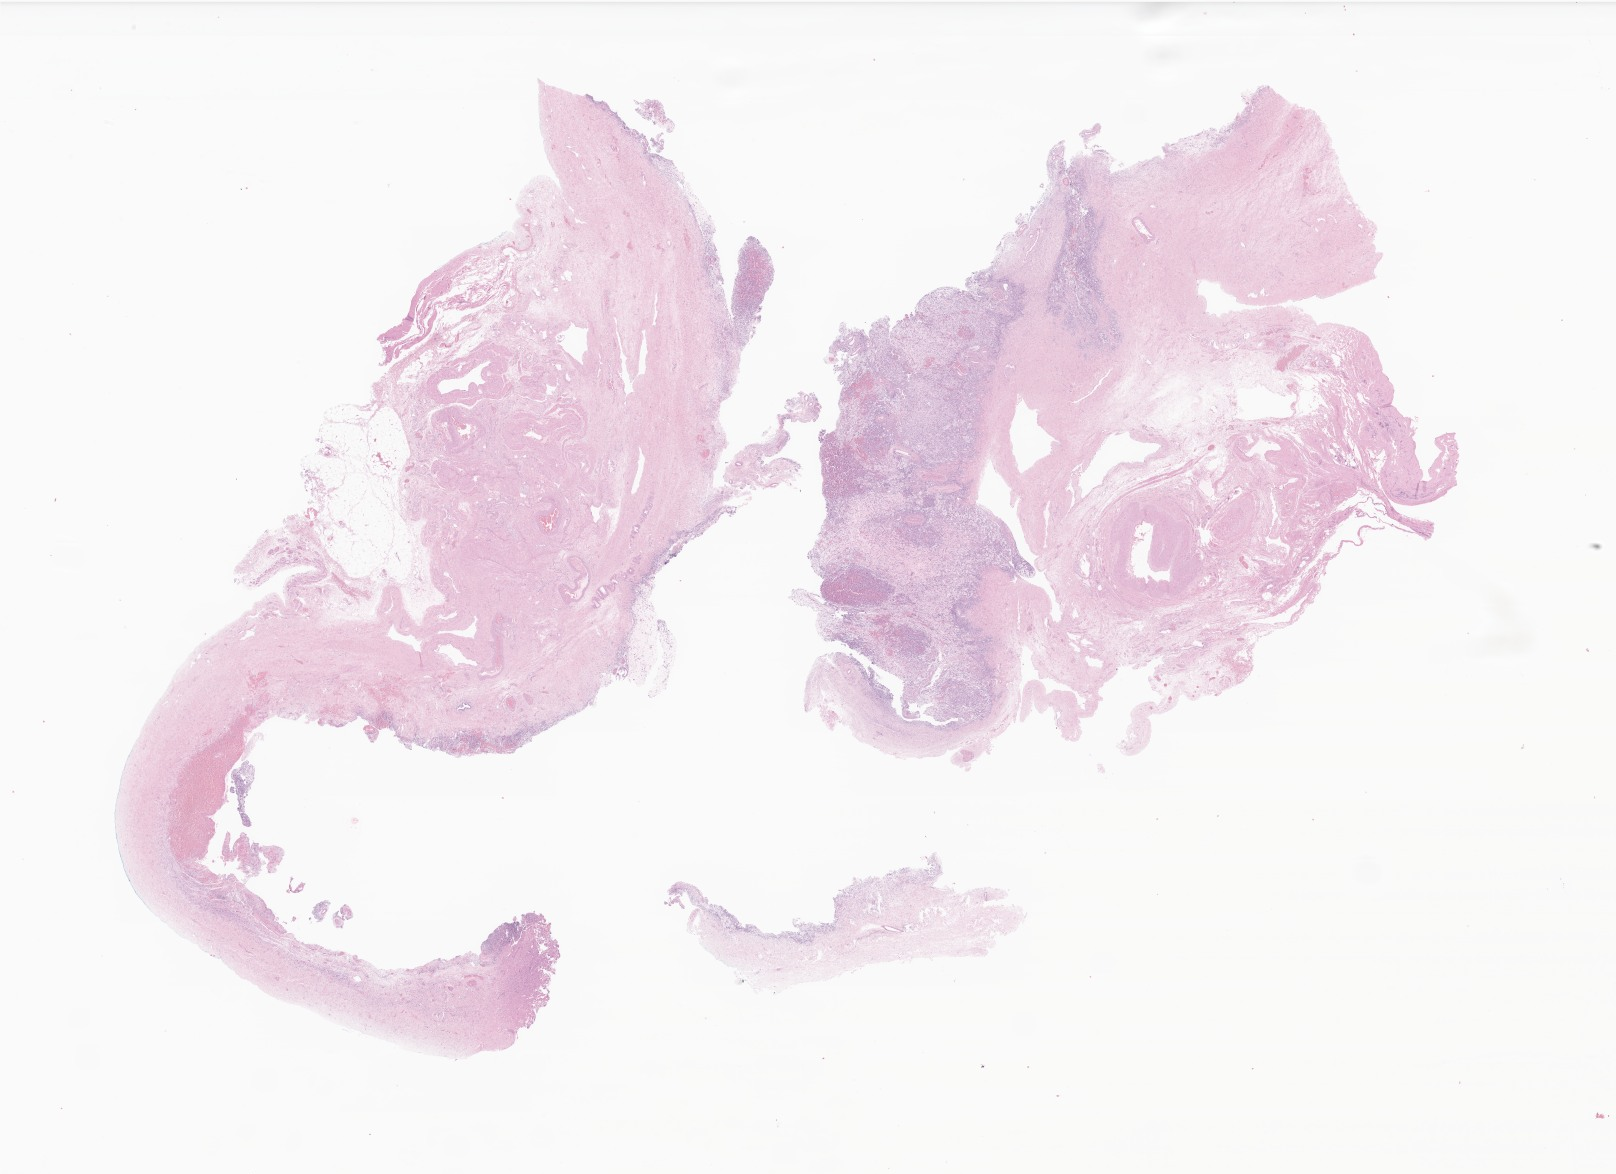
Digitized hematoxylin and eosin (H&E)-stained section of tumor tissue from the ovary, a low-resolution overview of the entire scanned area, about 27.3 x 19.8 mm; formalin-fixed paraffin-embedded section. Female patient, age 184 months.
* recorded diagnosis: Sex cord-gonadal stromal tumor, NOS